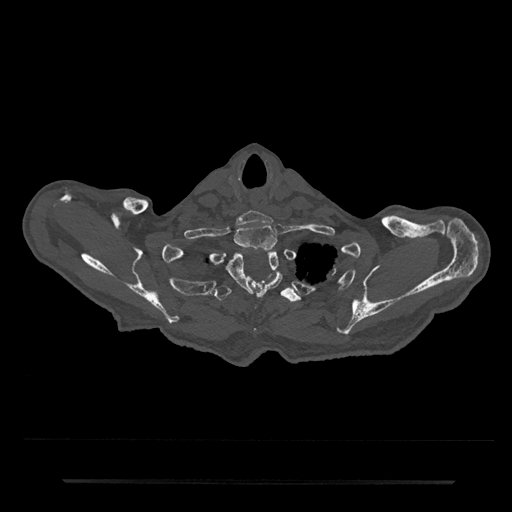
CT including the spine, one axial slice; position 694 of 797 along the scan axis; 120 kVp; bone window (W 1800 / L 400 HU); 0.5 mm slice thickness; 512 × 512 image matrix. Patient: male, 74 years. From the clinical record (not read from this slice): primary cancer: prostate.
Annotated regions visible in this slice (semi-automatically segmented with operator editing):
- T1 vertebra: box from (x=234, y=225) to (x=277, y=251) px
- T2 vertebra: (x=220, y=248)–(x=283, y=300)
- T3 vertebra: (x=214, y=273)–(x=301, y=303)